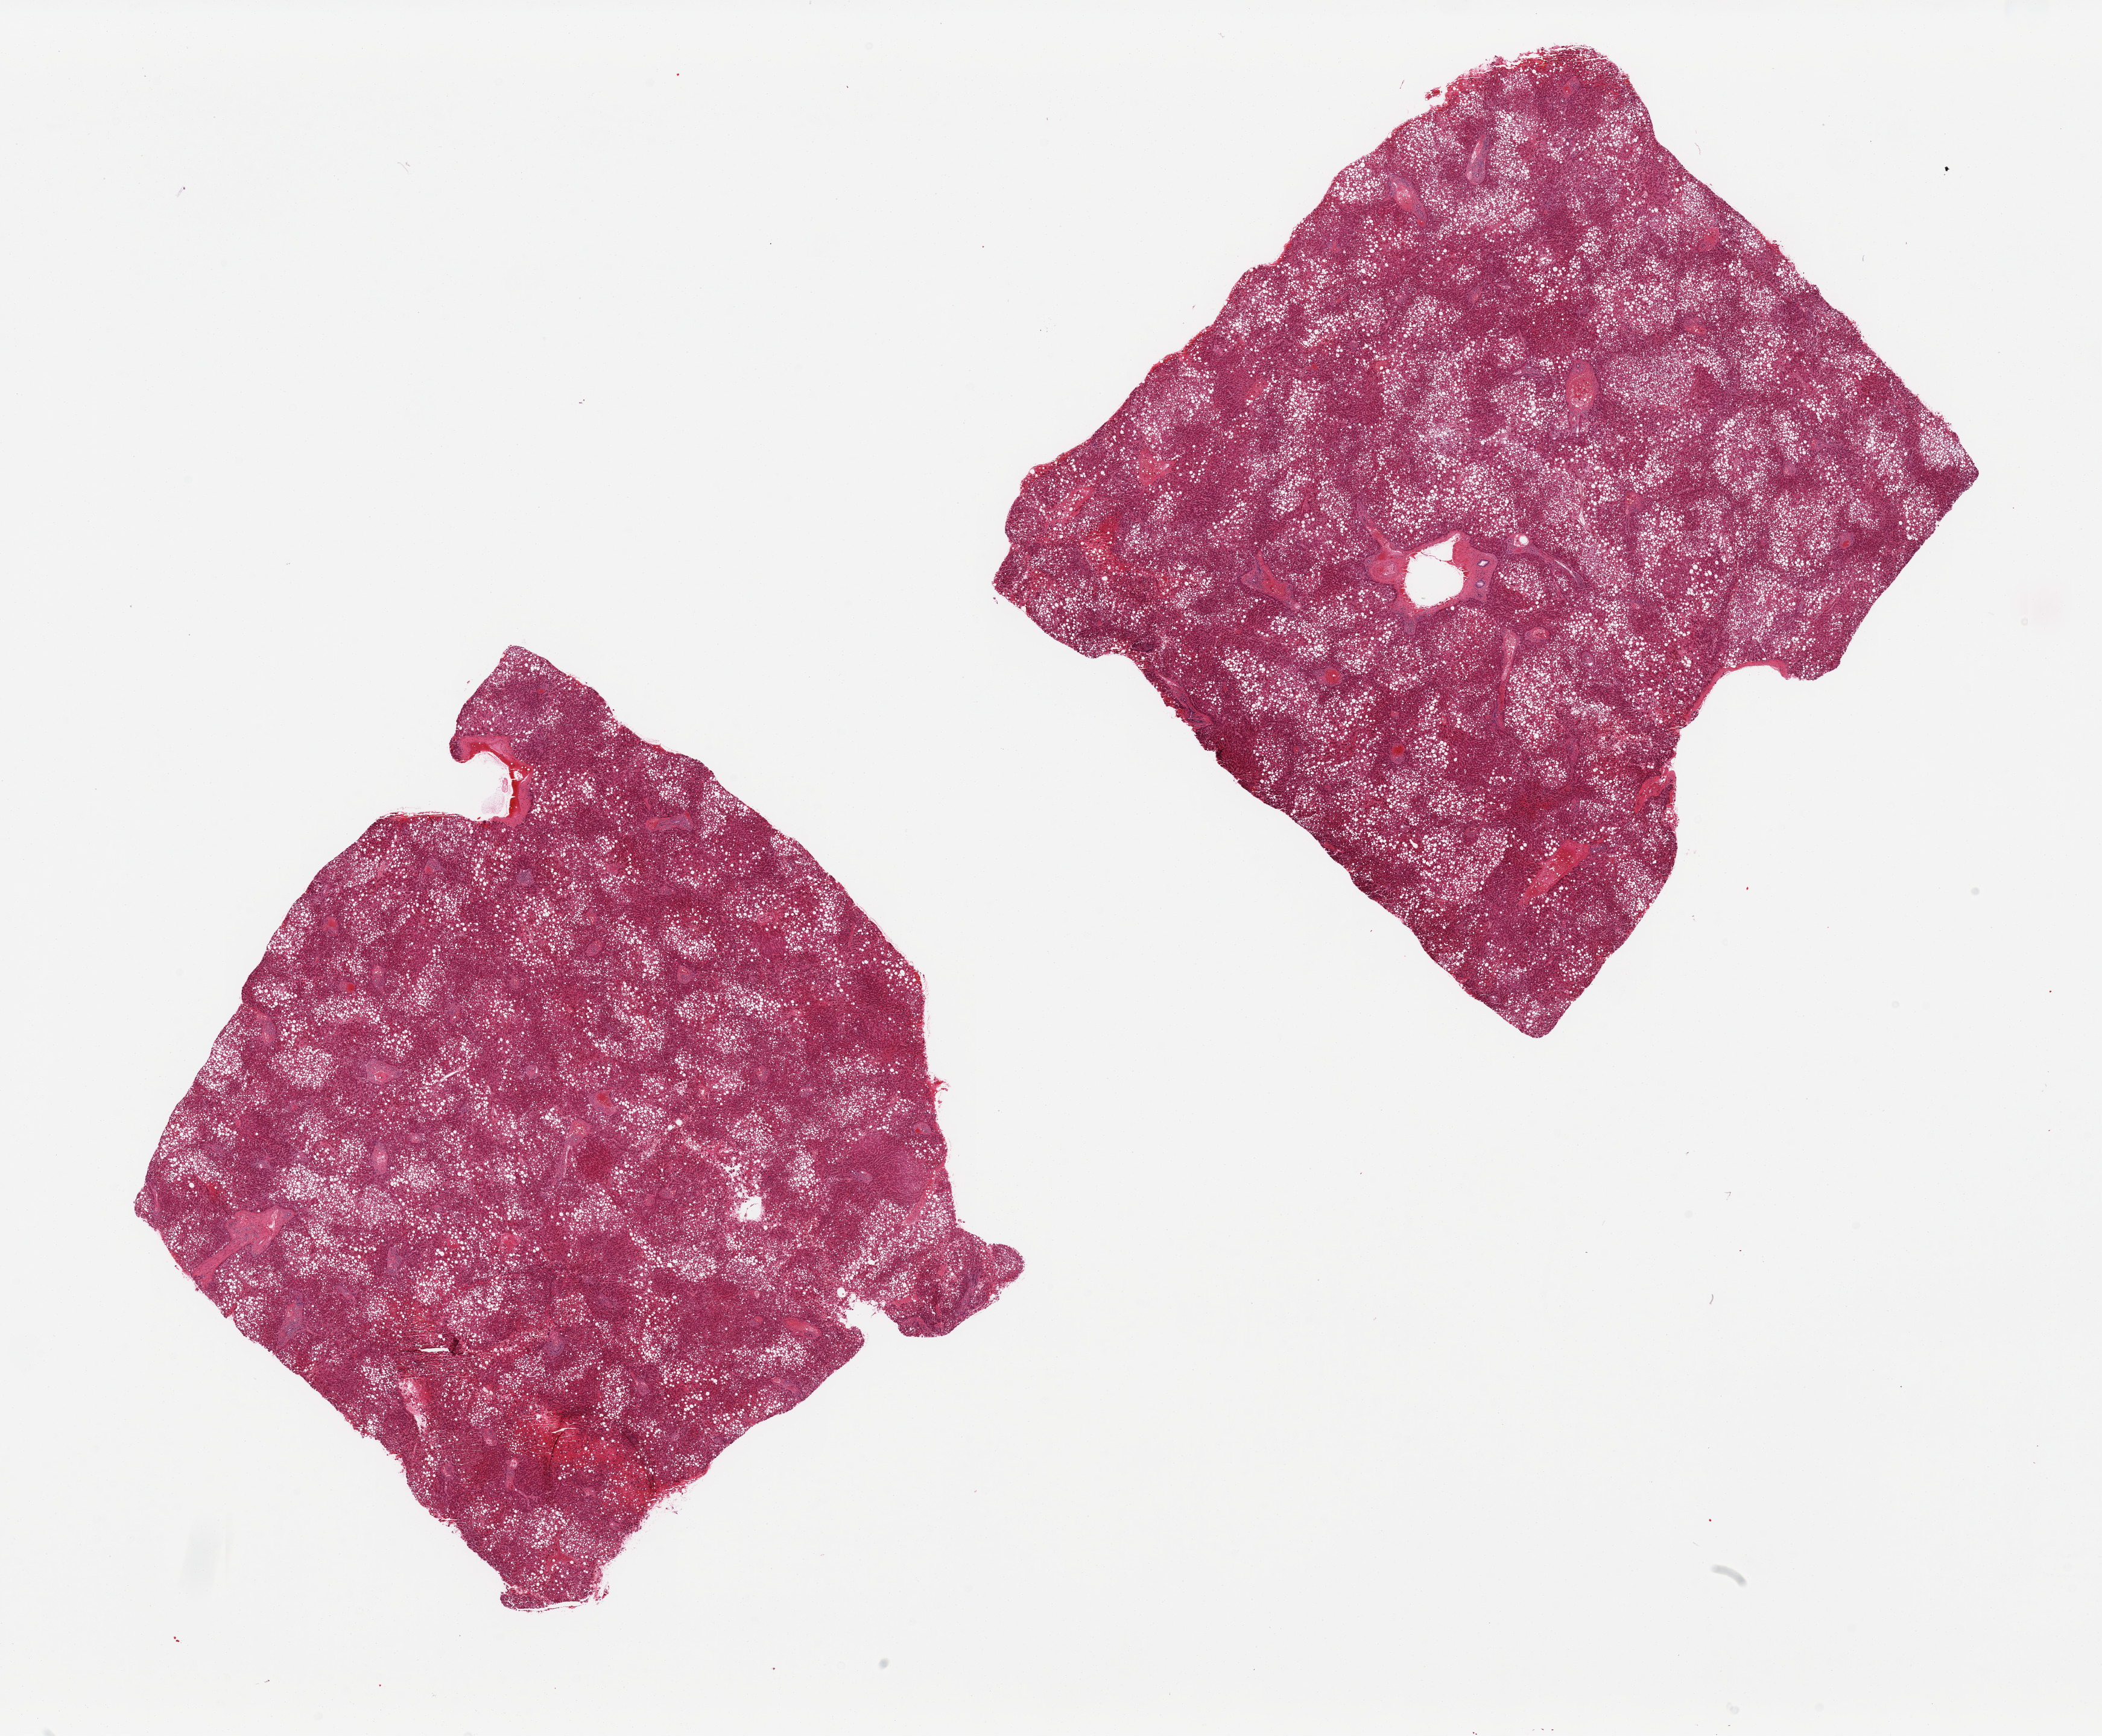
Digitized haematoxylin and eosin-stained section — low-resolution overview of the scanned area, about 27.6 x 22.8 mm. PAXgene-fixed, paraffin-embedded tissue. Section of liver (target tissue). Donor tissue sample. Male donor.
- pathologist's review note for this sample: 2 pieces, severe micro and macrovesicular steatosis